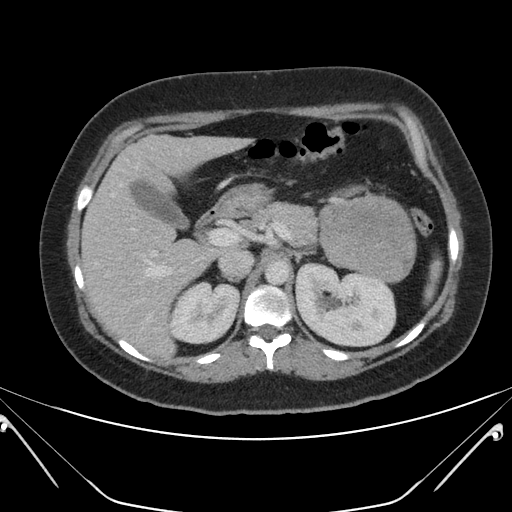
Contrast-enhanced abdominal CT, one axial slice; position 127 of 168 along the scan axis; 120 kVp; intravenous contrast given; soft-tissue window (W 400 / L 40 HU); 512 × 512 image matrix, field of view 394 × 394 mm. Female patient, age 26 years. From the clinical record (not read from this slice): diagnosis: adrenocortical carcinoma; tumour side: left adrenal; tumour size at pathology: 28 cm; Ki-67 index: 20 %; stage (as recorded): 2.
Outlined on this slice (semi-automatic segmentation, software-assisted and operator-edited):
- mass: bounding box <321,197,413,279> (left, top, right, bottom; pixels)